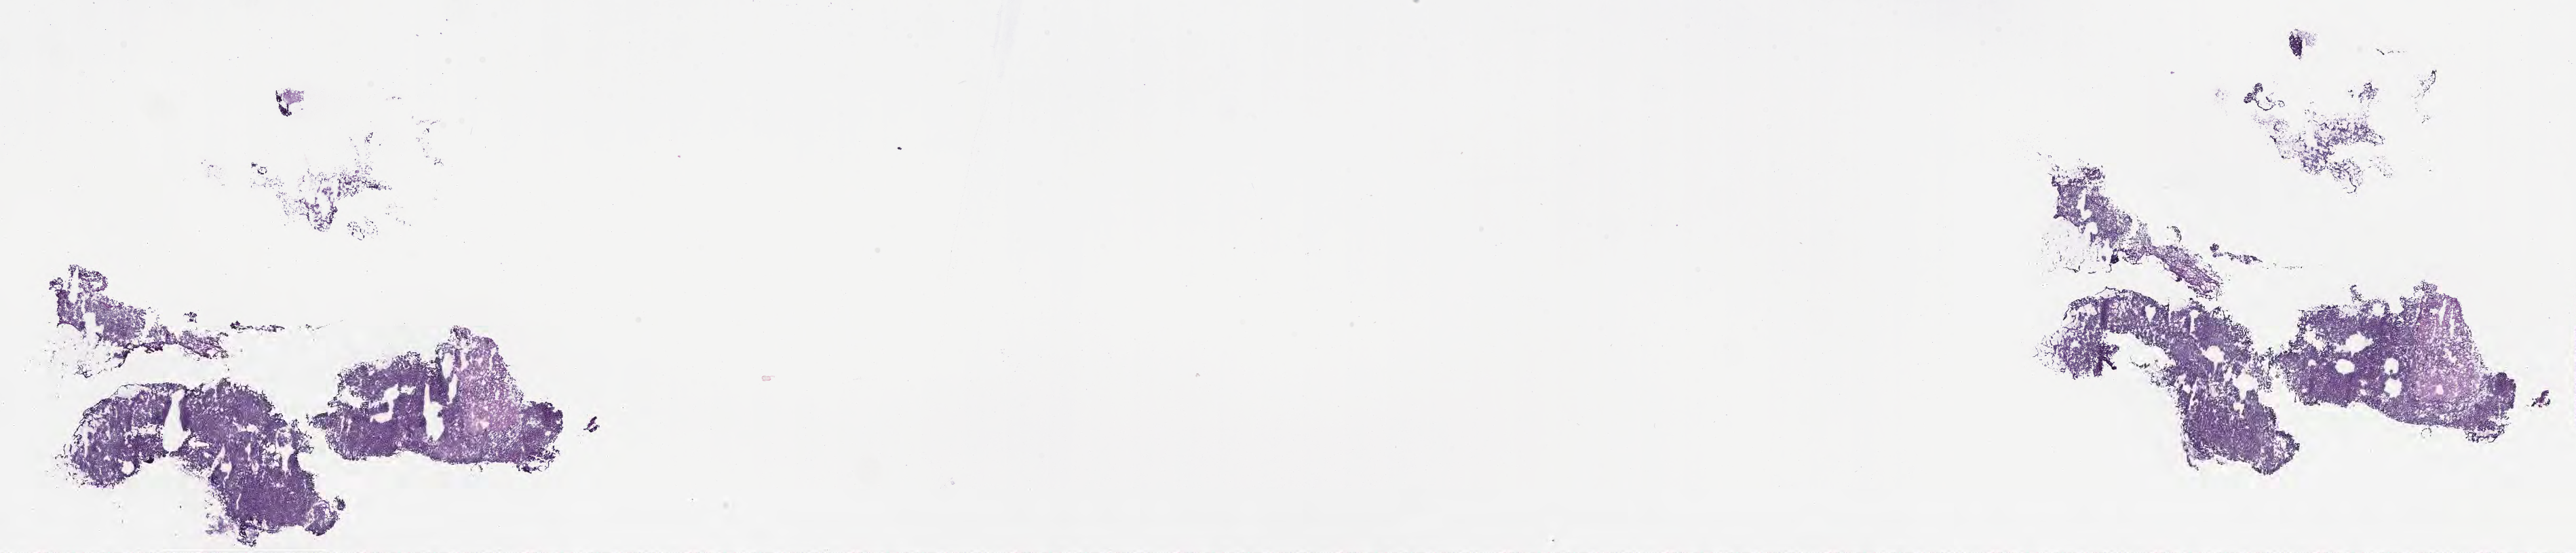
Hematoxylin and eosin (H&E) whole-slide image of tumor tissue from the cerebellum — shown as a low-resolution overview of the whole scanned area (about 30.7 x 6.6 mm); frozen section. Patient female; age 39 months (3 years 3 months).
Diagnosis (ICD-O-3 morphology term): Desmoplastic nodular medulloblastoma.